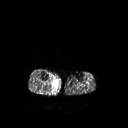
FDG PET of an extremity soft-tissue mass (from a PET/CT study), one axial slice; position 124 of 267 along the scan axis; 3.27 mm slice thickness; 128 × 128 image matrix, field of view 500 × 500 mm. Male patient, age 69 years. Case-level facts recorded for this patient, not image findings: histological type: pleiomorphic liposarcoma; grade: high; site of the primary tumour: right calf.
Annotated regions visible in this slice (expert contour drawn on MRI and transferred to this co-registered scan by the dataset authors):
- gross tumour volume including surrounding oedema: bounding box <51,79,59,90> (left, top, right, bottom; pixels)
- gross tumour volume (mass): <55,84,56,85>